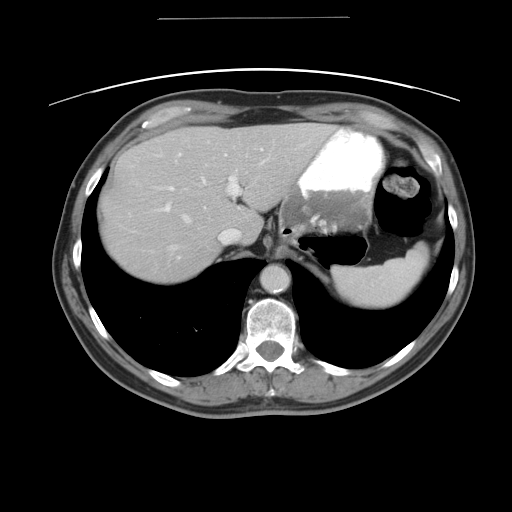
Contrast-enhanced abdominal CT, one axial slice. Slice 36 of 49 in the series (ordered by position). 120 kVp. Intravenous contrast given. Soft-tissue window (W 400 / L 40 HU). 512 × 512 image matrix, field of view 413 × 413 mm. Male patient, age 57 years. Case-level facts recorded for this patient, not image findings: diagnosis: colorectal cancer liver metastases, imaged before liver resection; multiple liver metastases: yes; largest metastasis: 4 cm.
Outlined on this slice (outlined manually by an expert reader):
- hepatic veins: bounding box [x1, y1, x2, y2] px = [168, 159, 263, 249]
- liver: [99, 123, 334, 283]
- planned liver remnant (the part of the liver to remain after resection): [207, 123, 333, 244]
- portal vein (with intrahepatic branches): [154, 140, 263, 212]